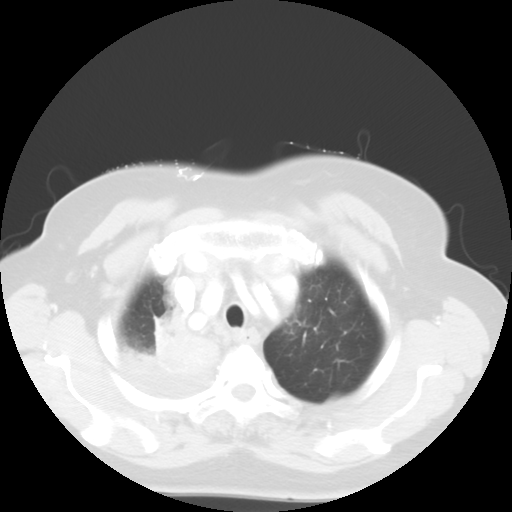
Chest CT, one axial slice; slice 45 of 52 in the series (ordered by position); 120 kVp; lung window (W 1500 / L -600 HU); 5 mm slice thickness; 512 × 512 image matrix, field of view 333 × 333 mm. Patient: female, 81 years. From the clinical record (not read from this slice): clinical TNM (as recorded): T4 N3 M1b.
Outlined on this slice (bounding box drawn by a radiologist):
- lung tumour (recorded histology: adenocarcinoma): bounding box (x1, y1, x2, y2) in pixels: (121, 318, 222, 386)